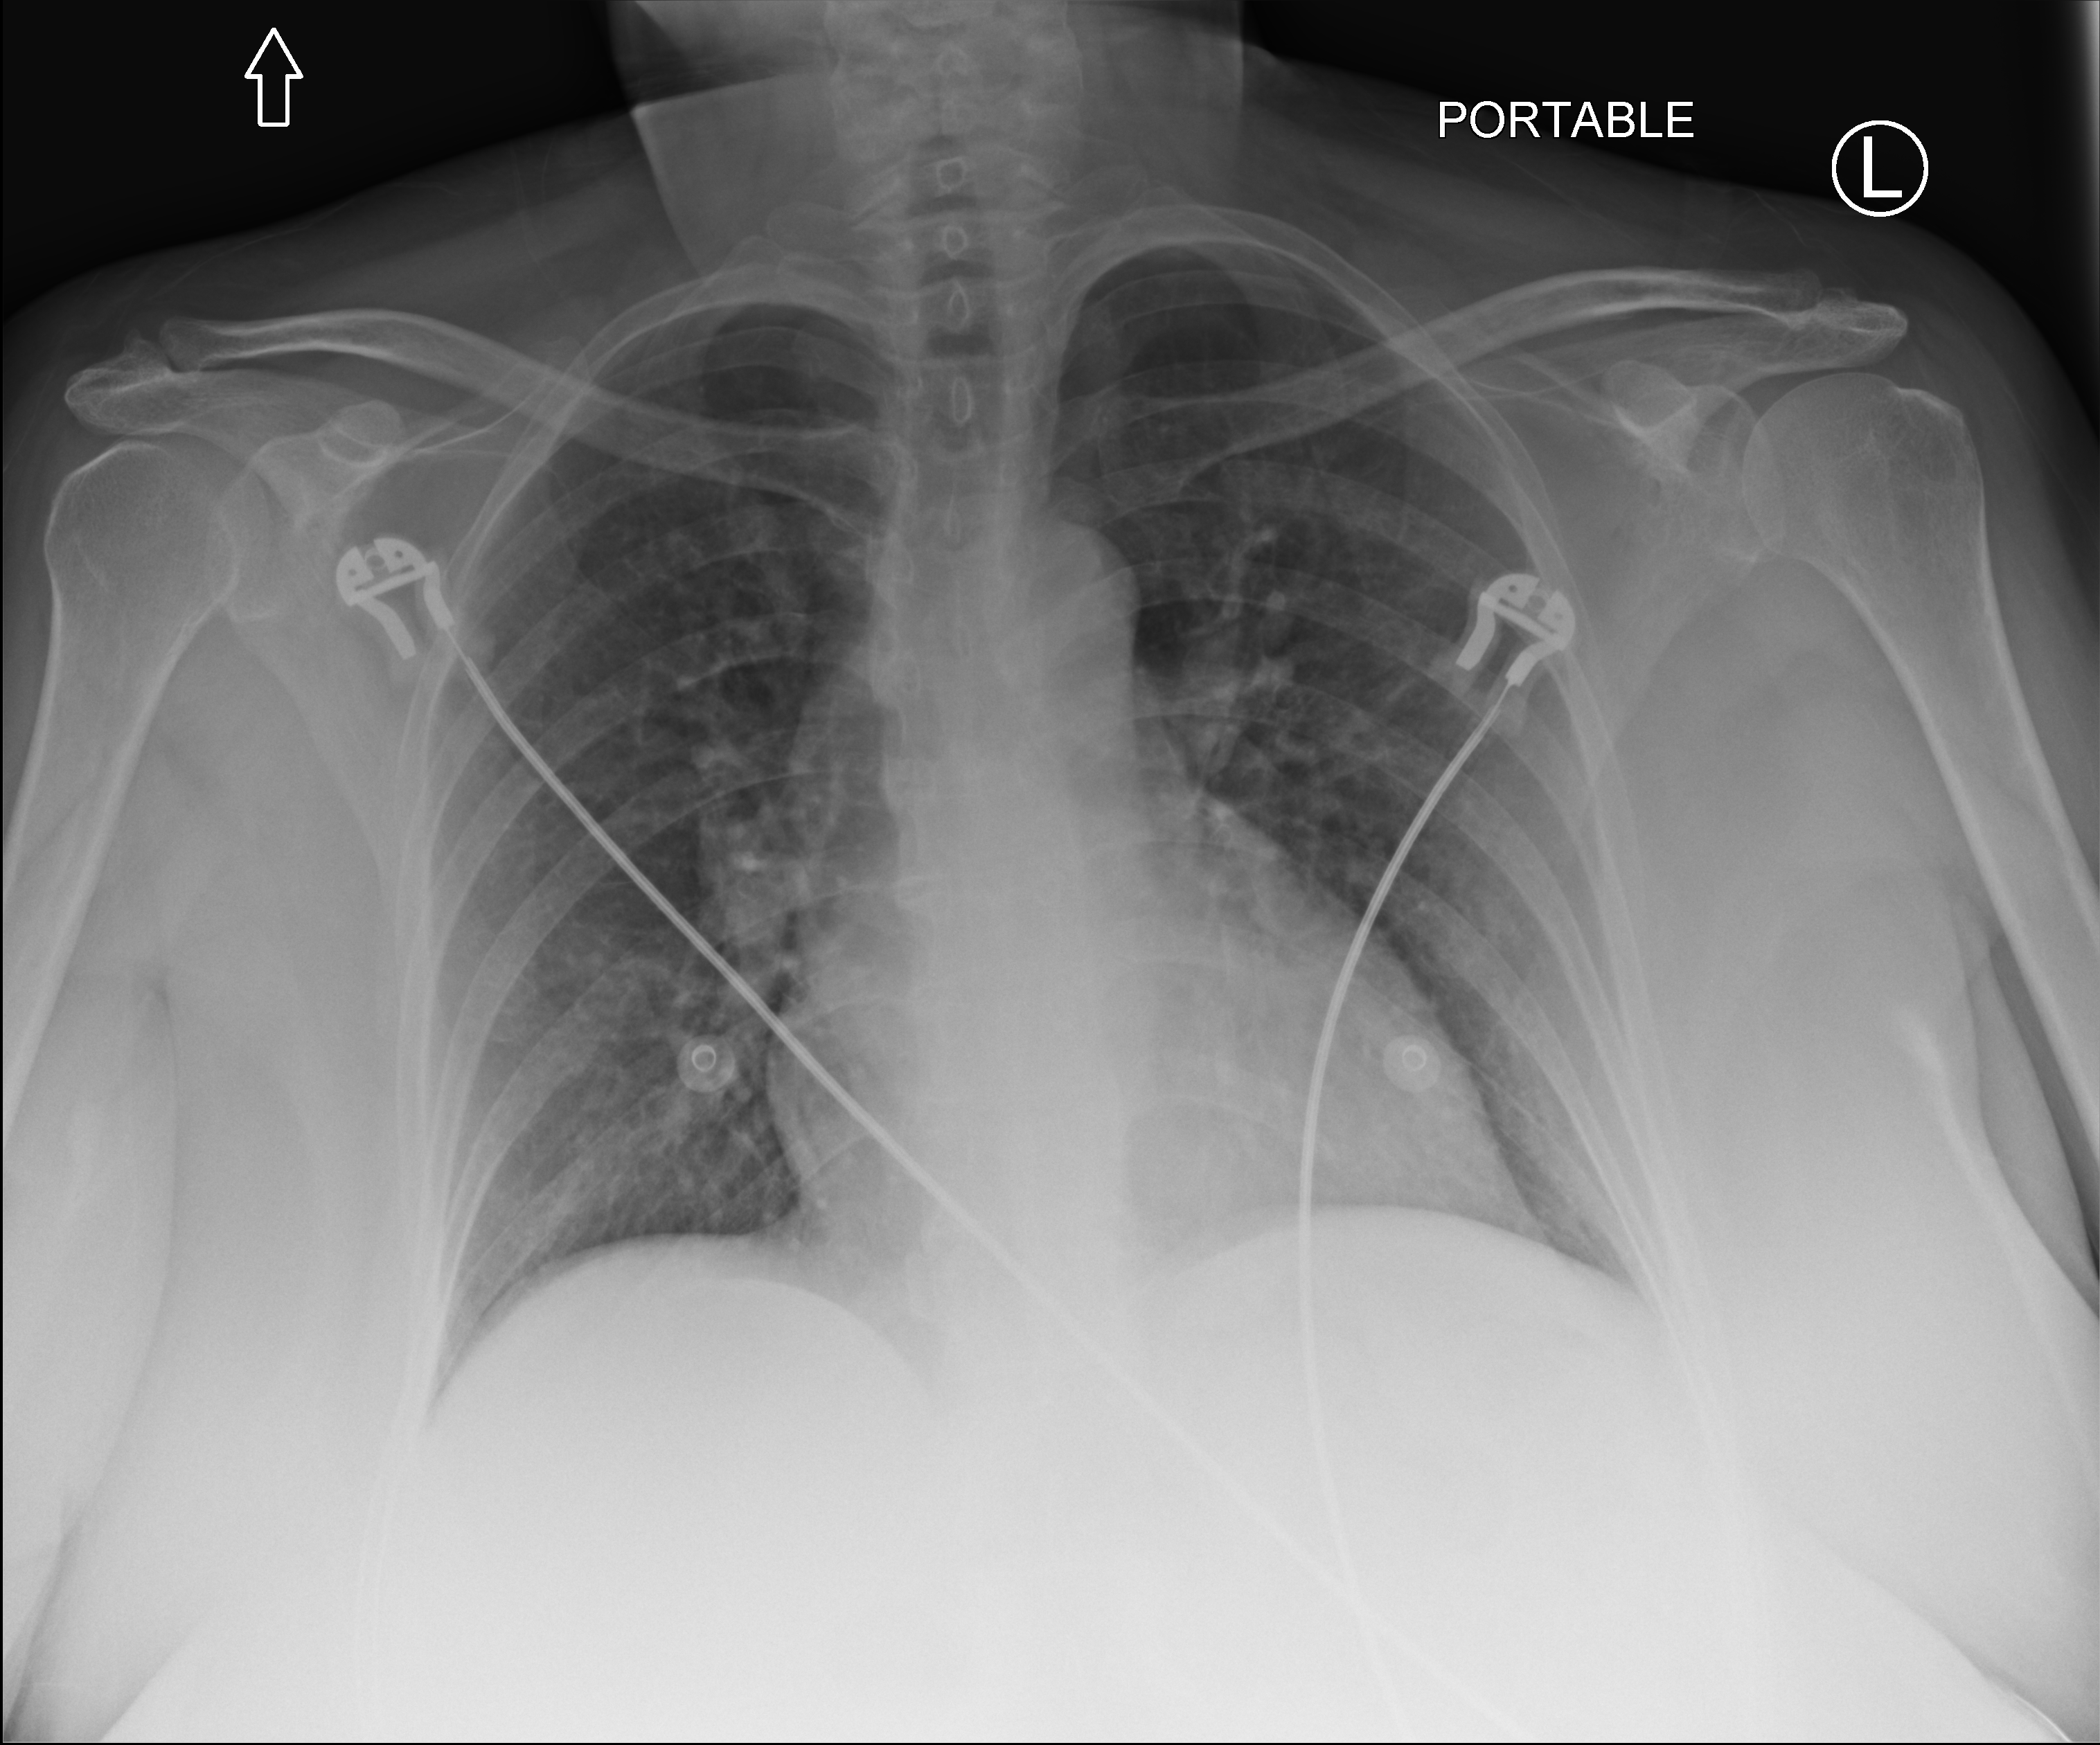
Chest X-ray (portable); anteroposterior (AP) projection. Patient hospitalised with COVID-19; female, aged 18–59 years.
From the hospital-stay record, not from the radiograph (when in the stay this image was taken is not recorded): other chronic lung disease (admission record): no.